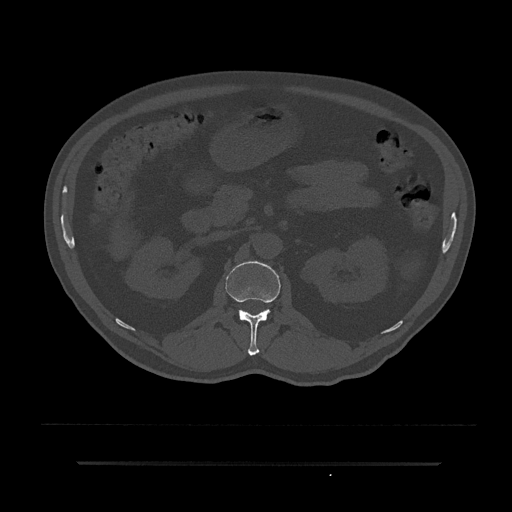
CT including the spine, one axial slice; slice 133 of 797 in the series (ordered by position); 120 kVp; bone window (W 1800 / L 400 HU); 0.5 mm slice thickness; 512 × 512 image matrix, field of view 464 × 464 mm. Male patient, age 59 years. From the clinical record (not read from this slice): primary cancer: bile ducts; vertebrae with lytic lesions (as recorded): T10.
Annotated regions visible in this slice (semi-automatic segmentation, software-assisted and operator-edited):
- L1 vertebra: bounding box (x1, y1, x2, y2) in pixels: (225, 261, 280, 356)